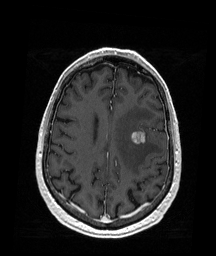
Brain MRI from a brain-tumour surgery series, one axial slice; position 65 of 176 along the scan axis; T1-weighted post-contrast; 1 mm slice thickness; 216 × 256 image matrix, field of view 211 × 250 mm. From the clinical record (not read from this slice): histopathology: Metastatic Melanoma; tumour location: Left Frontal.
Annotated regions visible in this slice (expert manual segmentation):
- tumour: bounding box <131,131,146,144> (left, top, right, bottom; pixels)